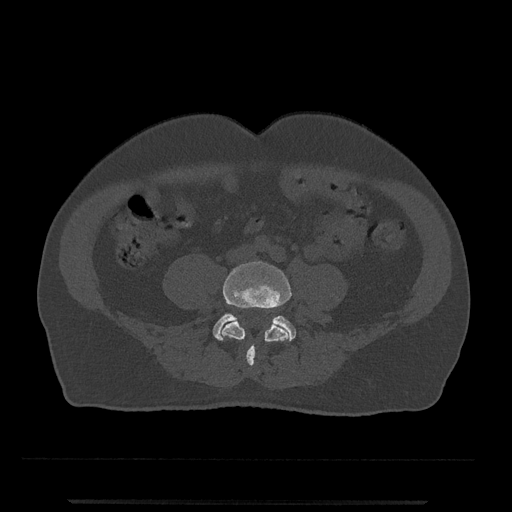
CT including the spine, one axial slice; position 110 of 797 along the scan axis; bone window (W 1800 / L 400 HU); 0.5 mm slice thickness; 512 × 512 image matrix. Male patient, age 63 years. Case-level facts recorded for this patient, not image findings: primary cancer: prostate.
Structures marked on this image (semi-automatically segmented with operator editing):
- L4 vertebra: box from (x=220, y=261) to (x=291, y=367) px
- L5 vertebra: (x=213, y=313)–(x=296, y=341)